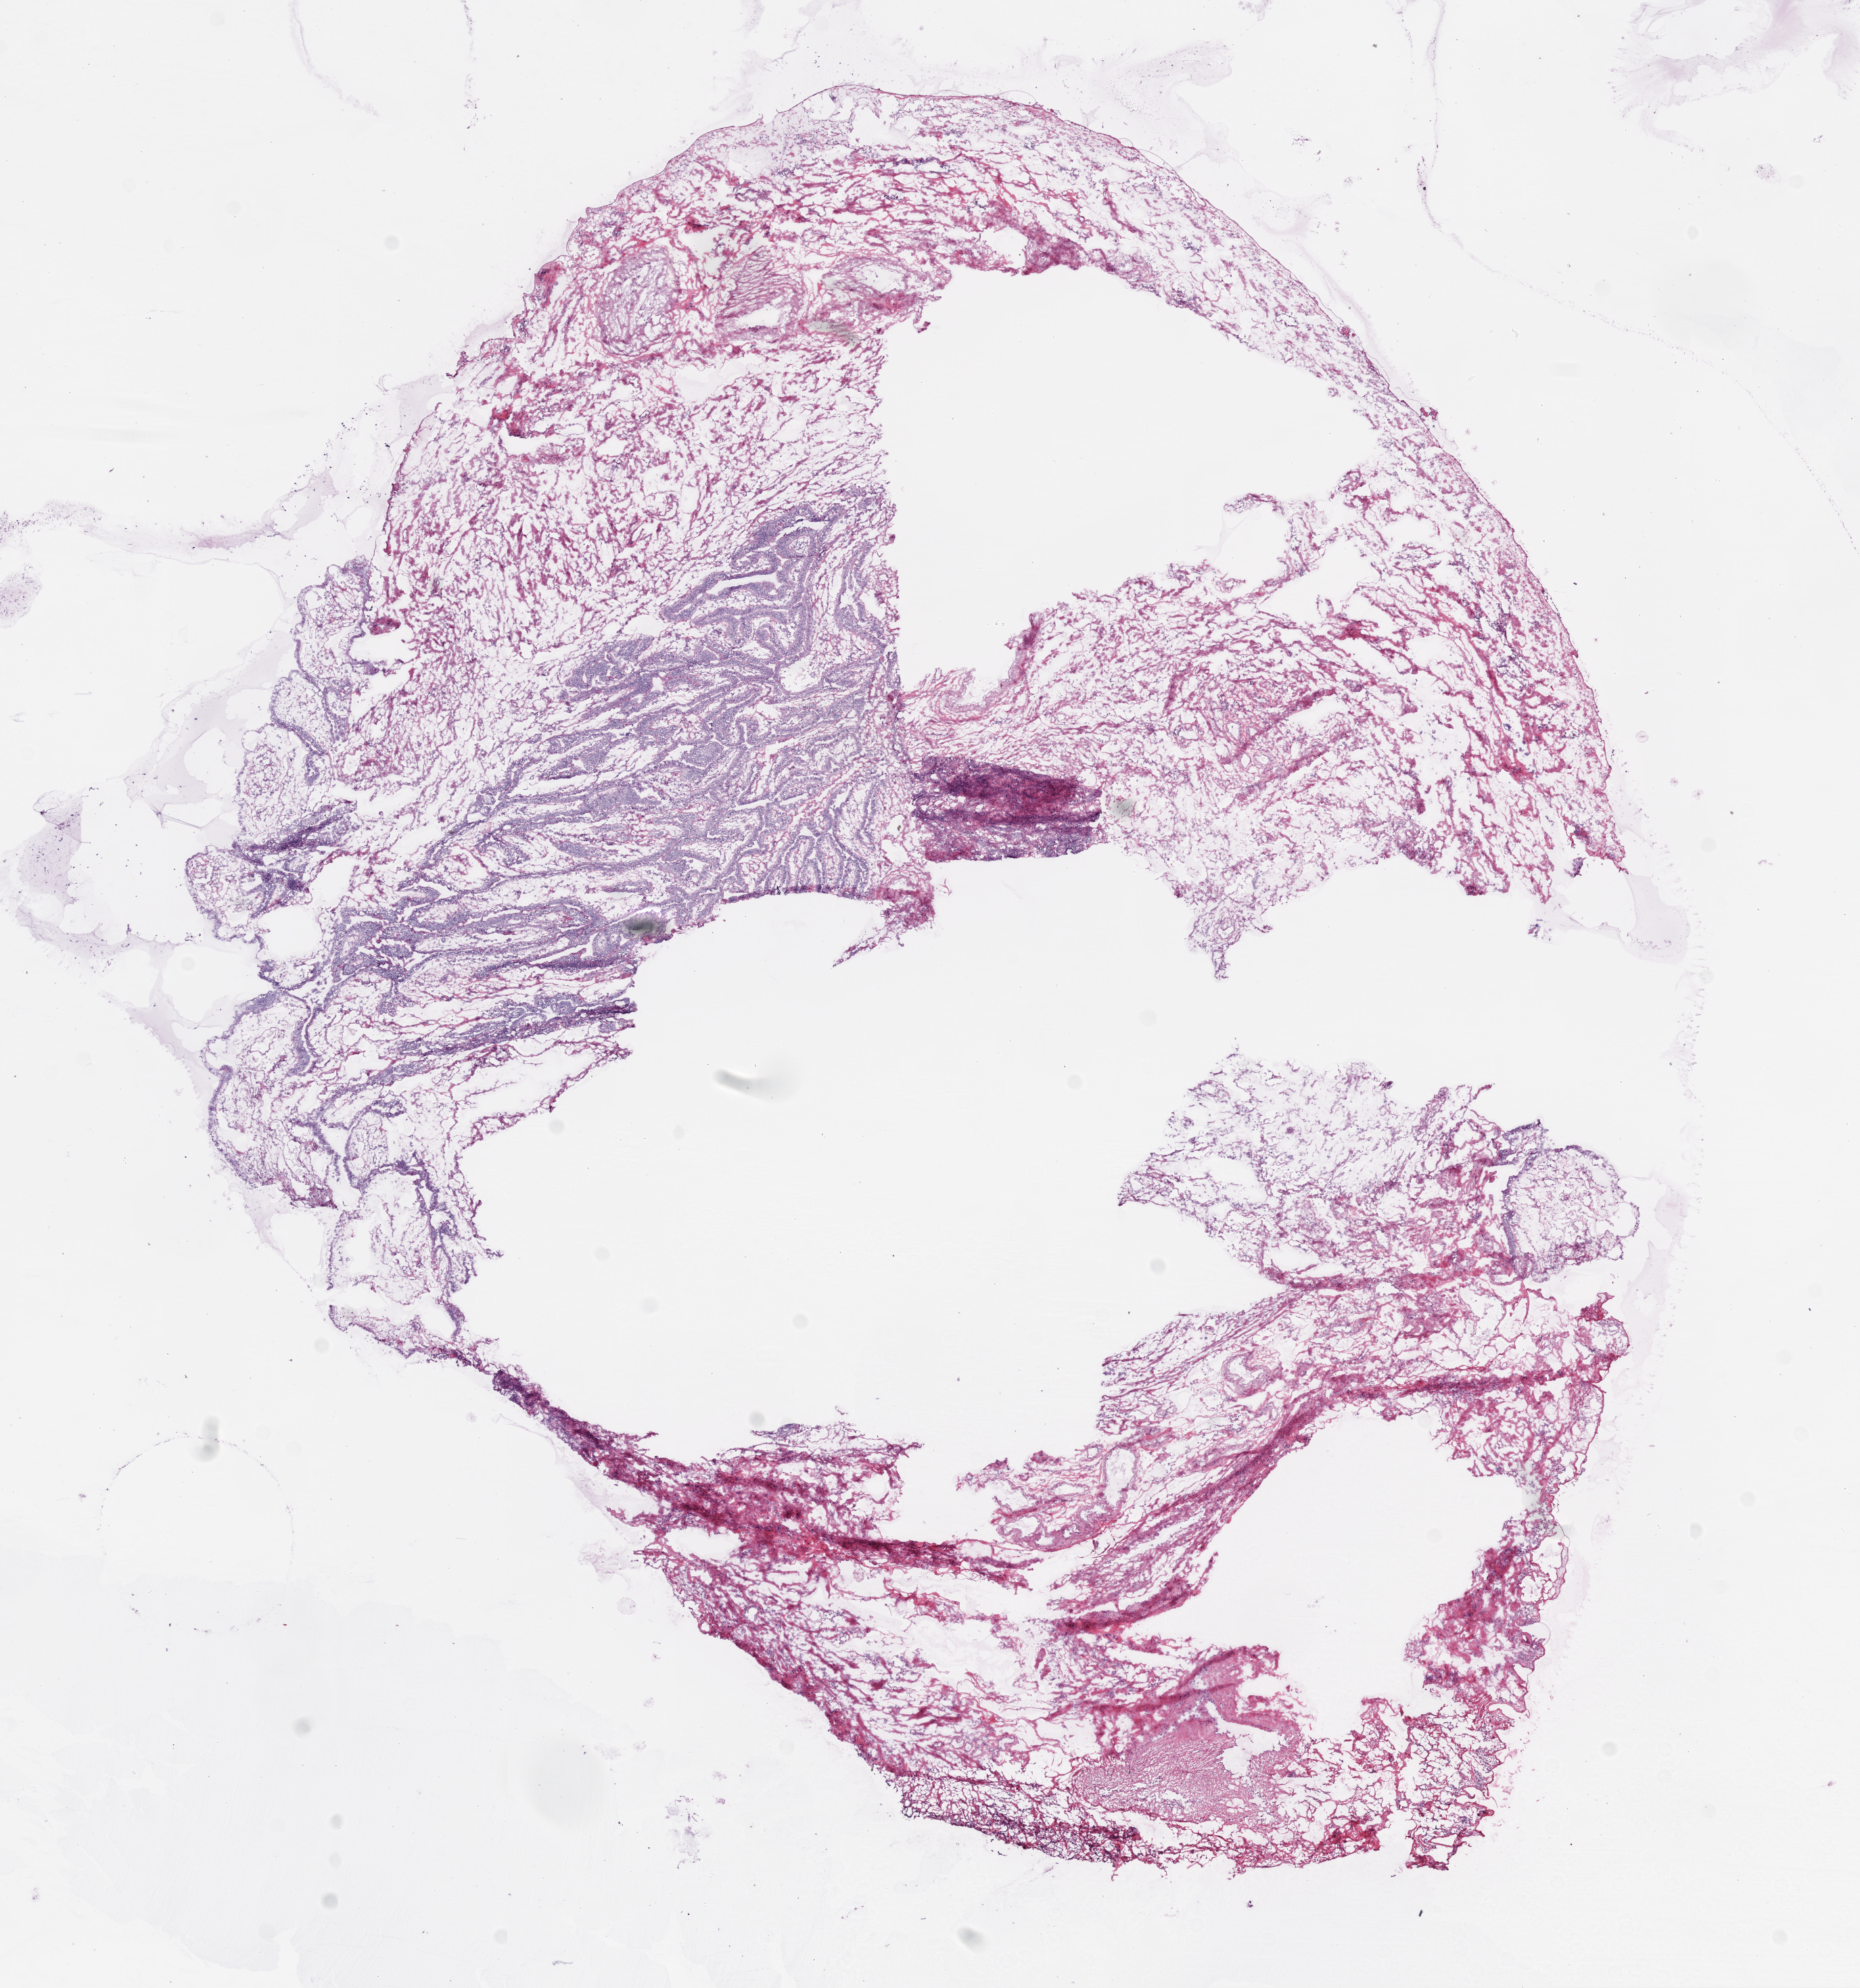
Digitized H&E-stained tissue section (whole slide), shown as a low-resolution overview of the whole scanned area (about 11.0 x 11.8 mm); frozen section from the bottom of the tissue portion; sample: solid tissue normal (non-tumour tissue), ovary. Female patient; age at initial diagnosis 49 years.
This section: solid tissue normal sample (biorepository sample class). Patient diagnosis: Serous cystadenocarcinoma, NOS.